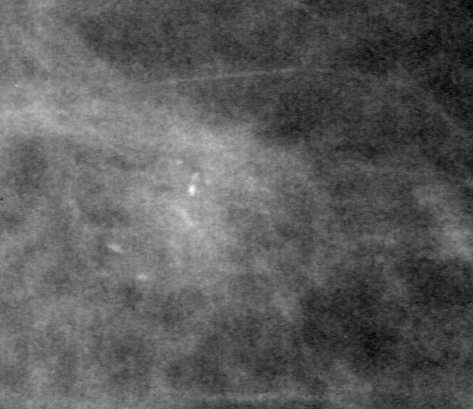
Region of interest cut from a scanned film mammogram (one marked finding); right breast; MLO view.
Calcifications, morphology pleomorphic, distribution clustered; BI-RADS assessment category 4; pathology (as recorded): malignant.